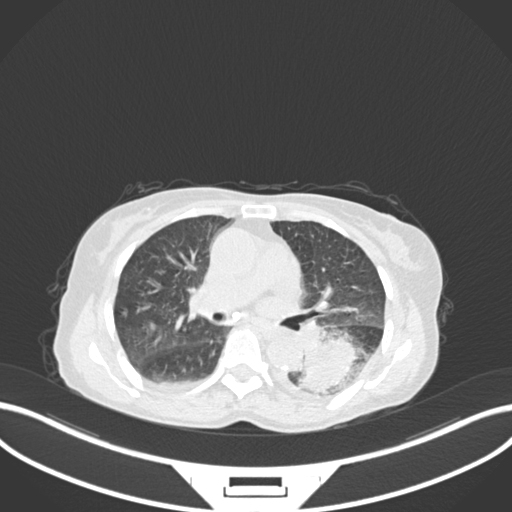
Chest CT, one axial slice; position 98 of 233 along the scan axis; lung window (W 1500 / L -600 HU); 1 mm slice thickness; 512 × 512 image matrix, field of view 400 × 400 mm. Patient: female, 78 years. Case-level facts recorded for this patient, not image findings: clinical TNM (as recorded): T3 N0 M1.
Structures marked on this image (bounding box drawn by a radiologist):
- lung tumour (recorded histology: squamous cell carcinoma): box from (x=294, y=337) to (x=366, y=397) px